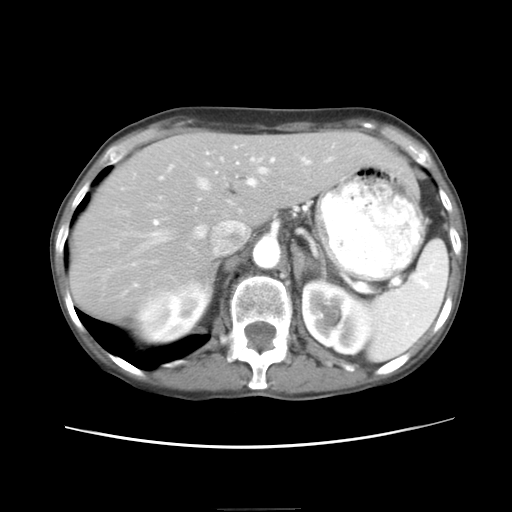
Contrast-enhanced abdominal CT, one axial slice; position 16 of 26 along the scan axis; reconstruction kernel STANDARD; soft-tissue window (W 400 / L 40 HU); 7.5 mm slice thickness; 512 × 512 image matrix, field of view 340 × 340 mm. Female patient, age 65 years. From the clinical record (not read from this slice): diagnosis: colorectal cancer liver metastases, imaged before liver resection; multiple liver metastases: no.
Structures marked on this image (expert manual segmentation):
- hepatic veins: bounding box [x1, y1, x2, y2] px = [150, 157, 310, 243]
- liver: [70, 132, 394, 317]
- planned liver remnant (the part of the liver to remain after resection): [70, 132, 393, 318]
- portal vein (with intrahepatic branches): [153, 146, 274, 235]
- liver metastasis: [360, 139, 371, 147]